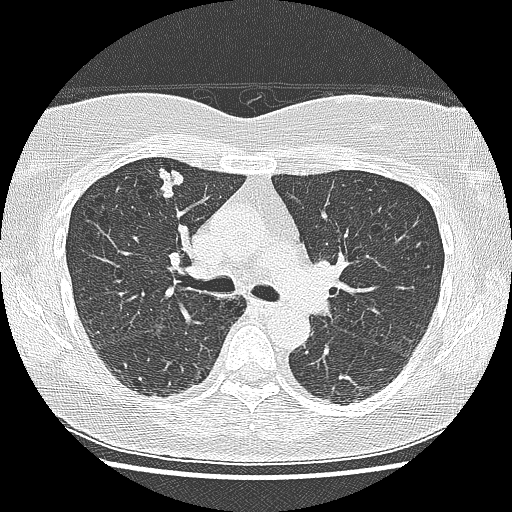
Low-dose screening chest CT, one axial slice. Slice 95 of 155 in the series (ordered by position). Reconstruction kernel LUNG. 120 kVp. Lung window (W 1500 / L -600 HU). 512 × 512 image matrix.
Outlined on this slice (manually delineated by an expert):
- lesion 1 (tumor, upper lobe of right lung): box from (x=156, y=168) to (x=183, y=198) px